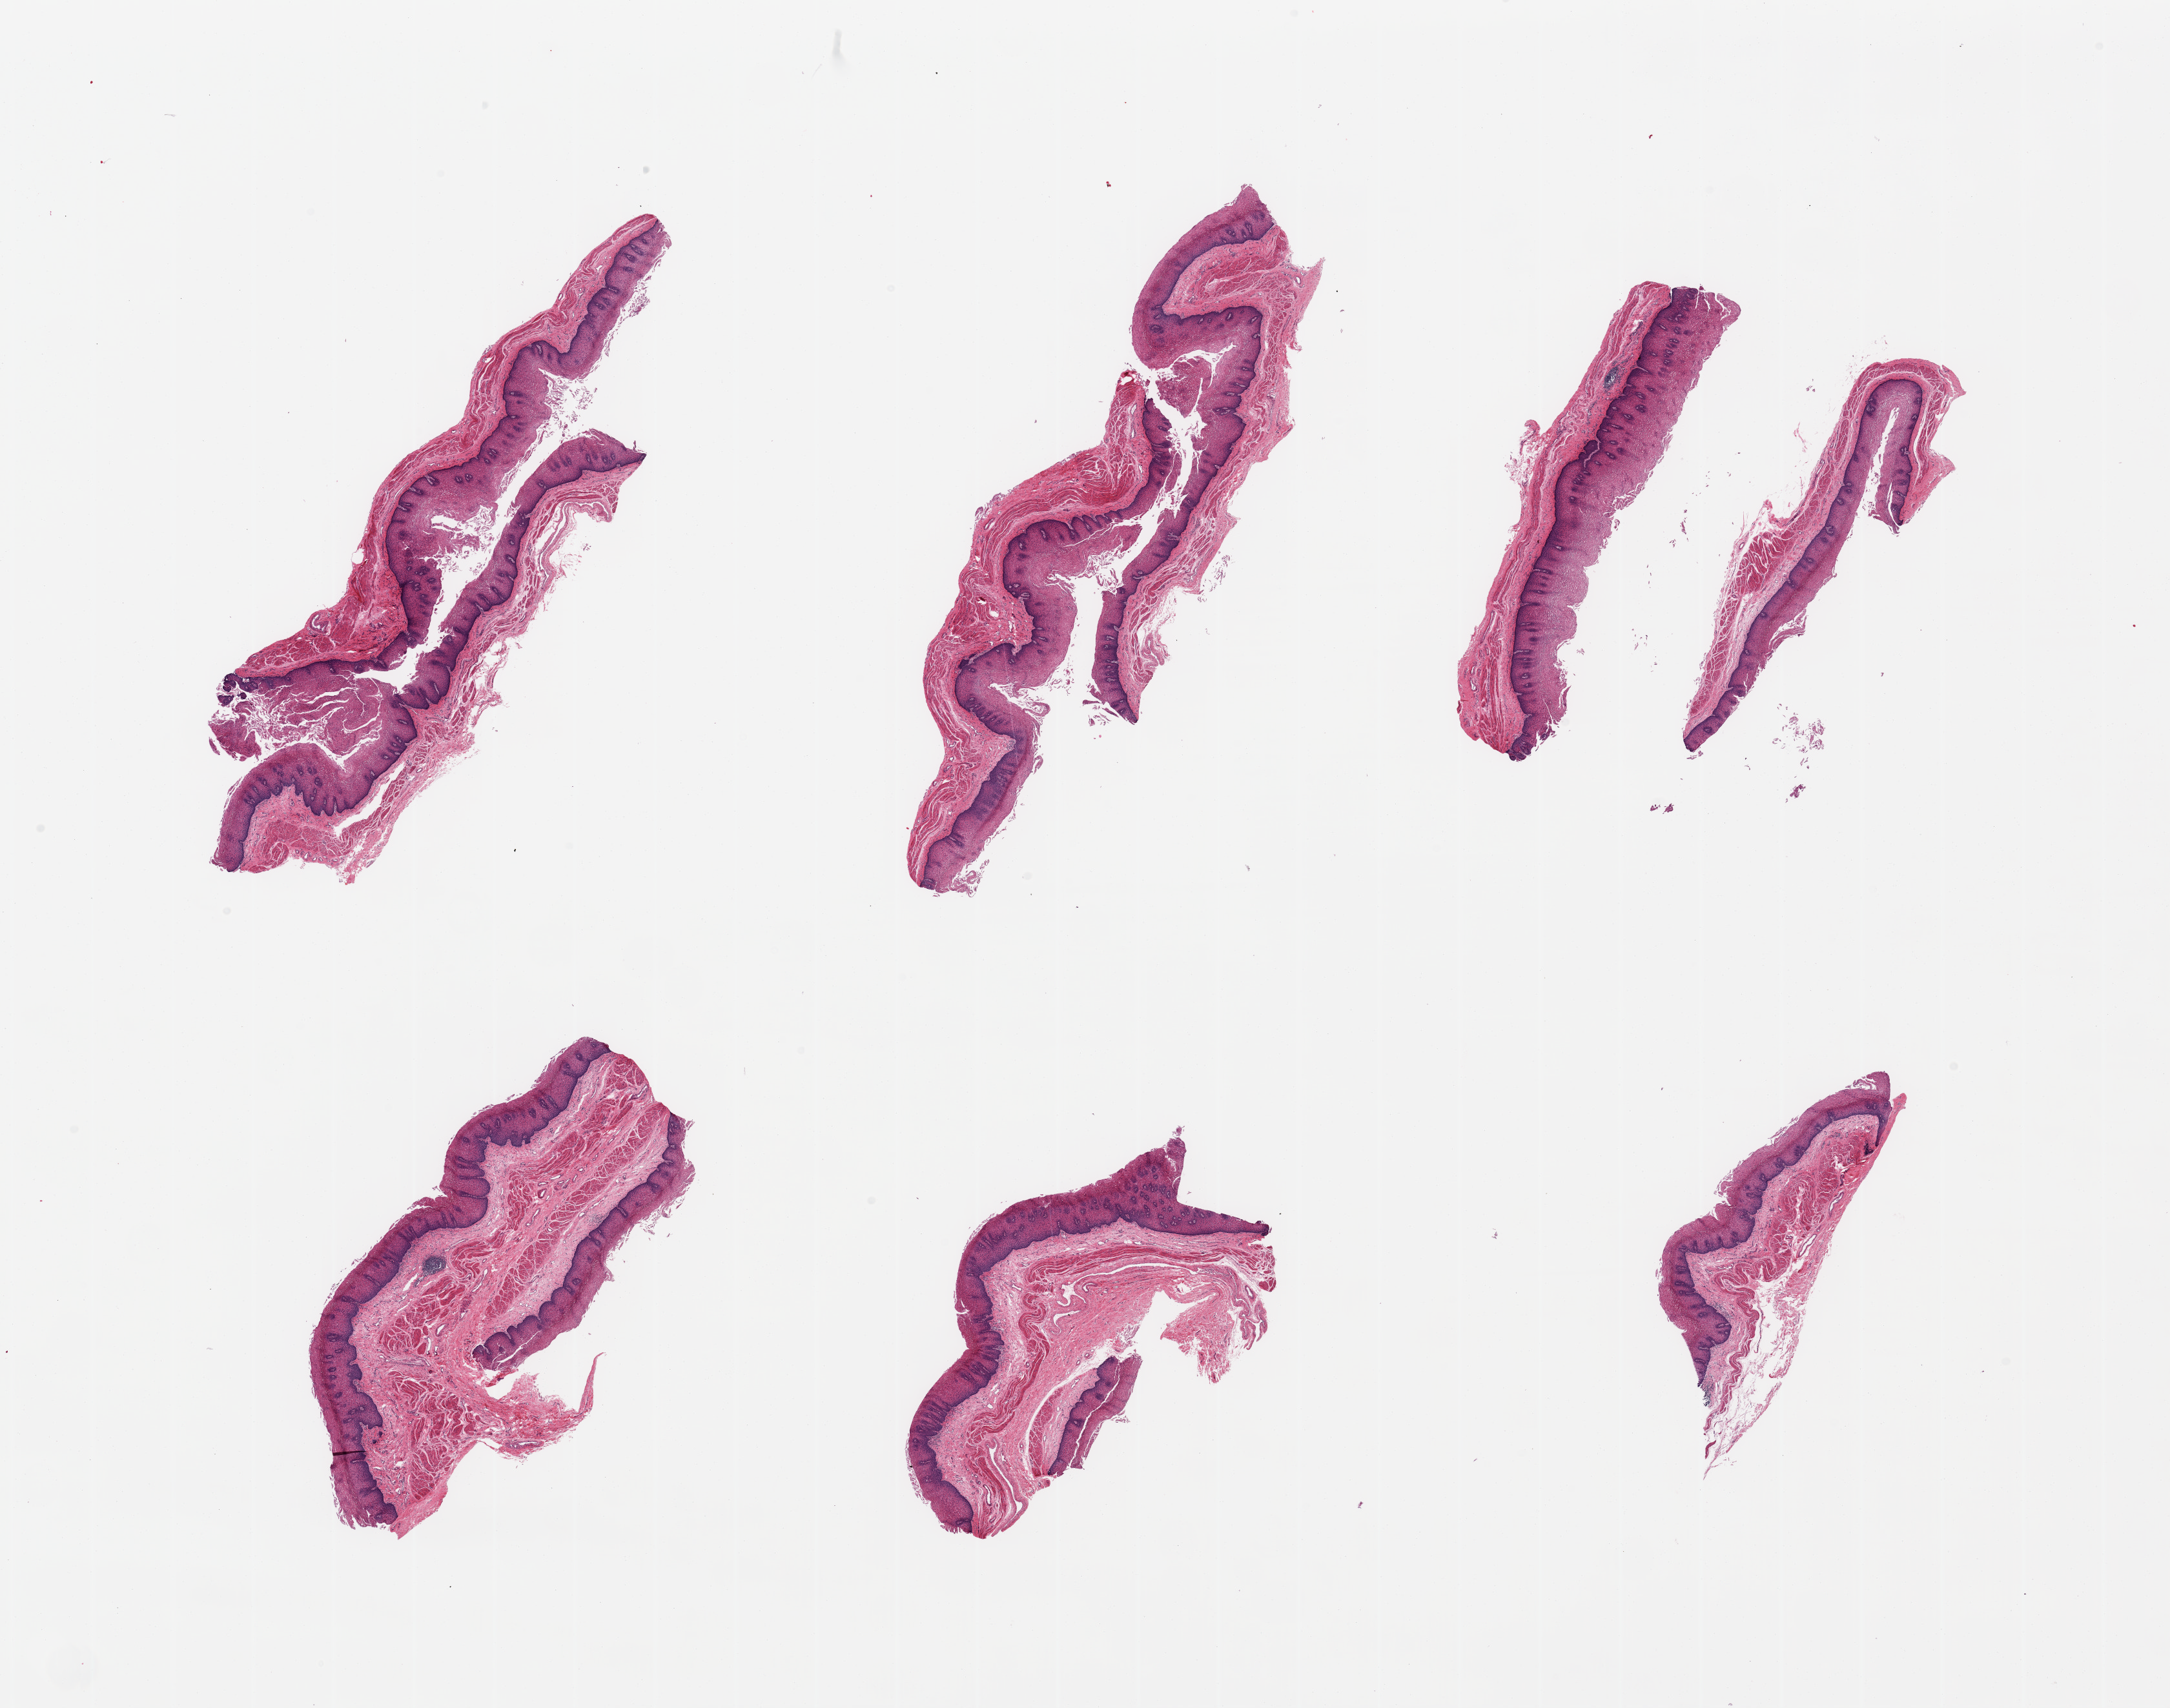
Haematoxylin and eosin whole-slide image, whole scanned area (about 26.6 x 20.9 mm, from a 20x scan) shown as a low-resolution overview; PAXgene-fixed paraffin-embedded (PFPE) section; target tissue: esophageal mucous membrane; tissue donor sample.
Review note (as recorded): 9 pieces, ~squamous mucosa up to ~0.5mm, ~30% of thickness.